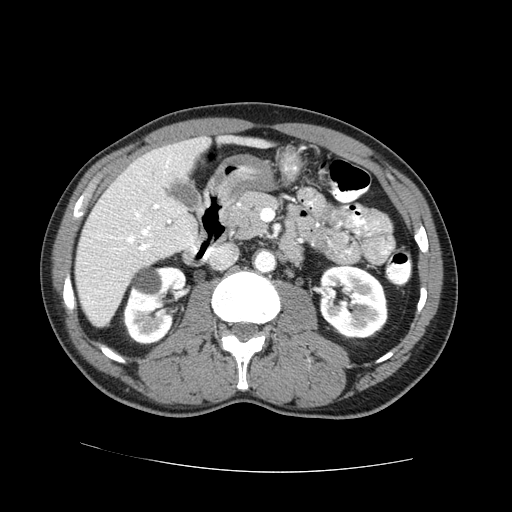
Contrast-enhanced abdominal CT (liver protocol), one axial slice. Position 27 of 73 along the scan axis. Reconstruction kernel STANDARD. One of 2 acquisitions stored at this slice position. Soft-tissue window (W 400 / L 40 HU). 512 × 512 image matrix. Case-level facts recorded for this patient, not image findings: diagnosis: hepatocellular carcinoma (patient treated with transarterial chemoembolisation; whether this scan precedes or follows treatment is not stated here); TNM stage (as recorded): Stage-IVA; Child-Pugh class: A.
Structures marked on this image (semi-automatically segmented with operator editing):
- liver parenchyma outside the tumour (the mass and vessels are separate outlines, so this box may not span the whole liver): box from (x=74, y=136) to (x=262, y=326) px
- liver vessels: (x=110, y=159)–(x=195, y=251)